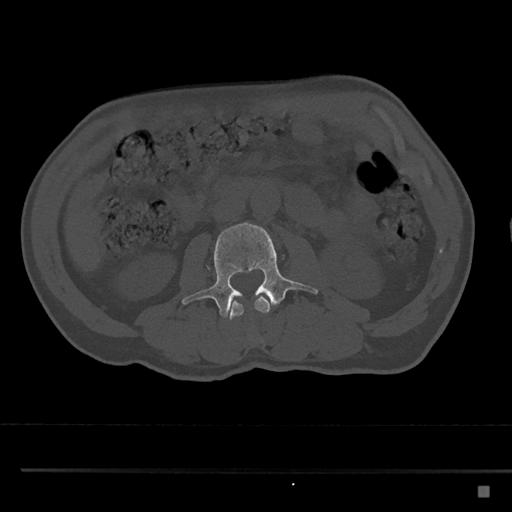
CT including the spine, one axial slice. Position 712 of 797 along the scan axis. Reconstruction kernel Br40s/3. Bone window (W 1800 / L 400 HU). 512 × 512 image matrix, field of view 391 × 391 mm. Male patient, age 59 years. Case-level facts recorded for this patient, not image findings: primary cancer: prostate.
Outlined on this slice (semi-automatically segmented with operator editing):
- L2 vertebra: bounding box [x1, y1, x2, y2] px = [228, 295, 270, 320]
- L3 vertebra: [181, 222, 318, 318]